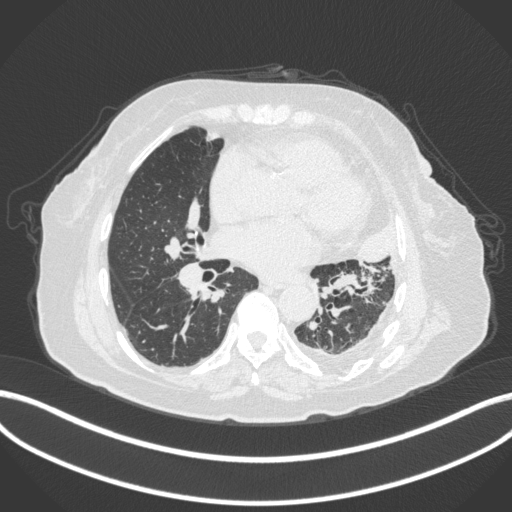
Chest CT, one axial slice. Position 172 of 399 along the scan axis. Reconstruction kernel B31f. Lung window (W 1500 / L -600 HU). 1 mm slice thickness. 512 × 512 image matrix, field of view 400 × 400 mm. Patient: female, 75 years. Case-level facts recorded for this patient, not image findings: clinical TNM (as recorded): T3 N3 M1.
Outlined on this slice (rectangle marked by the reading radiologist):
- lung tumour (recorded histology: adenocarcinoma): bounding box (x1, y1, x2, y2) in pixels: (351, 217, 395, 274)